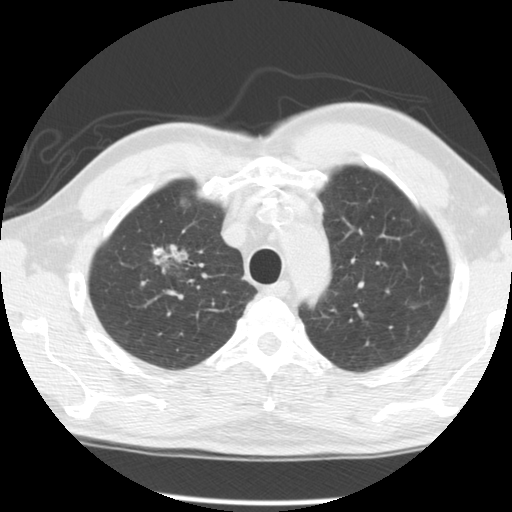
Chest CT (low-dose screening protocol), one axial image; second screening round (one year after baseline); lung window (W 1500 / L -600 HU); standard (soft-tissue) reconstruction kernel (STANDARD); slice 24 of 120 in the series. Male participant, aged 64 years at enrolment.
Lesion marked by an expert reader, bounding box [x1, y1, x2, y2] px = [121, 219, 206, 295]. The screening reader recorded 2 non-calcified nodules or masses ≥4 mm on this exam; which of them this box marks is not recorded. Participant outcome: lung cancer diagnosed 429 days after this screen (after the third annual screen) — adenocarcinoma, NOS, right upper lobe, well differentiated (G1), stage IB (AJCC 6th edition), 45 mm at pathology.